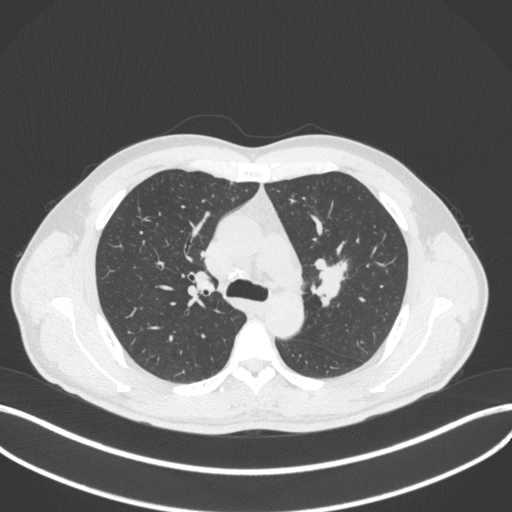
Chest CT, one axial slice; position 282 of 383 along the scan axis; lung window (W 1500 / L -600 HU); 1 mm slice thickness; 512 × 512 image matrix, field of view 400 × 400 mm. Patient: male, 50 years. From the clinical record (not read from this slice): clinical TNM (as recorded): T1c N1 M1b.
Outlined on this slice (bounding box drawn by a radiologist):
- lung tumour (recorded histology: squamous cell carcinoma): bounding box [x1, y1, x2, y2] px = [309, 253, 352, 311]